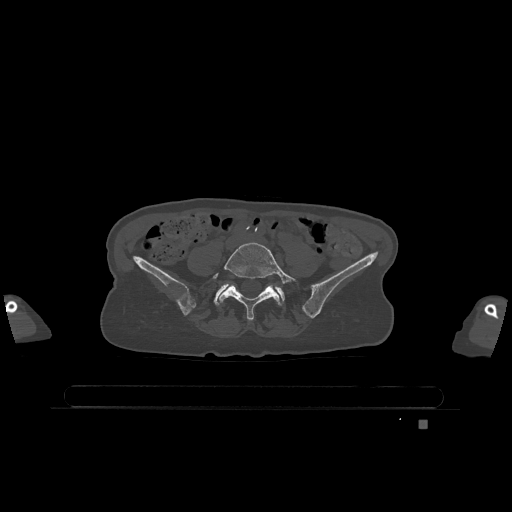
CT including the spine, one axial slice; slice 236 of 1317 in the series (ordered by position); bone window (W 1800 / L 400 HU); 512 × 512 image matrix, field of view 500 × 500 mm. Female patient, age 74 years. Case-level facts recorded for this patient, not image findings: primary cancer: lung; vertebrae with lytic lesions (as recorded): T1, T4, T5, T6, L4, L5.
Structures marked on this image (semi-automatically segmented with operator editing):
- L5 vertebra: bounding box [x1, y1, x2, y2] px = [213, 242, 296, 320]